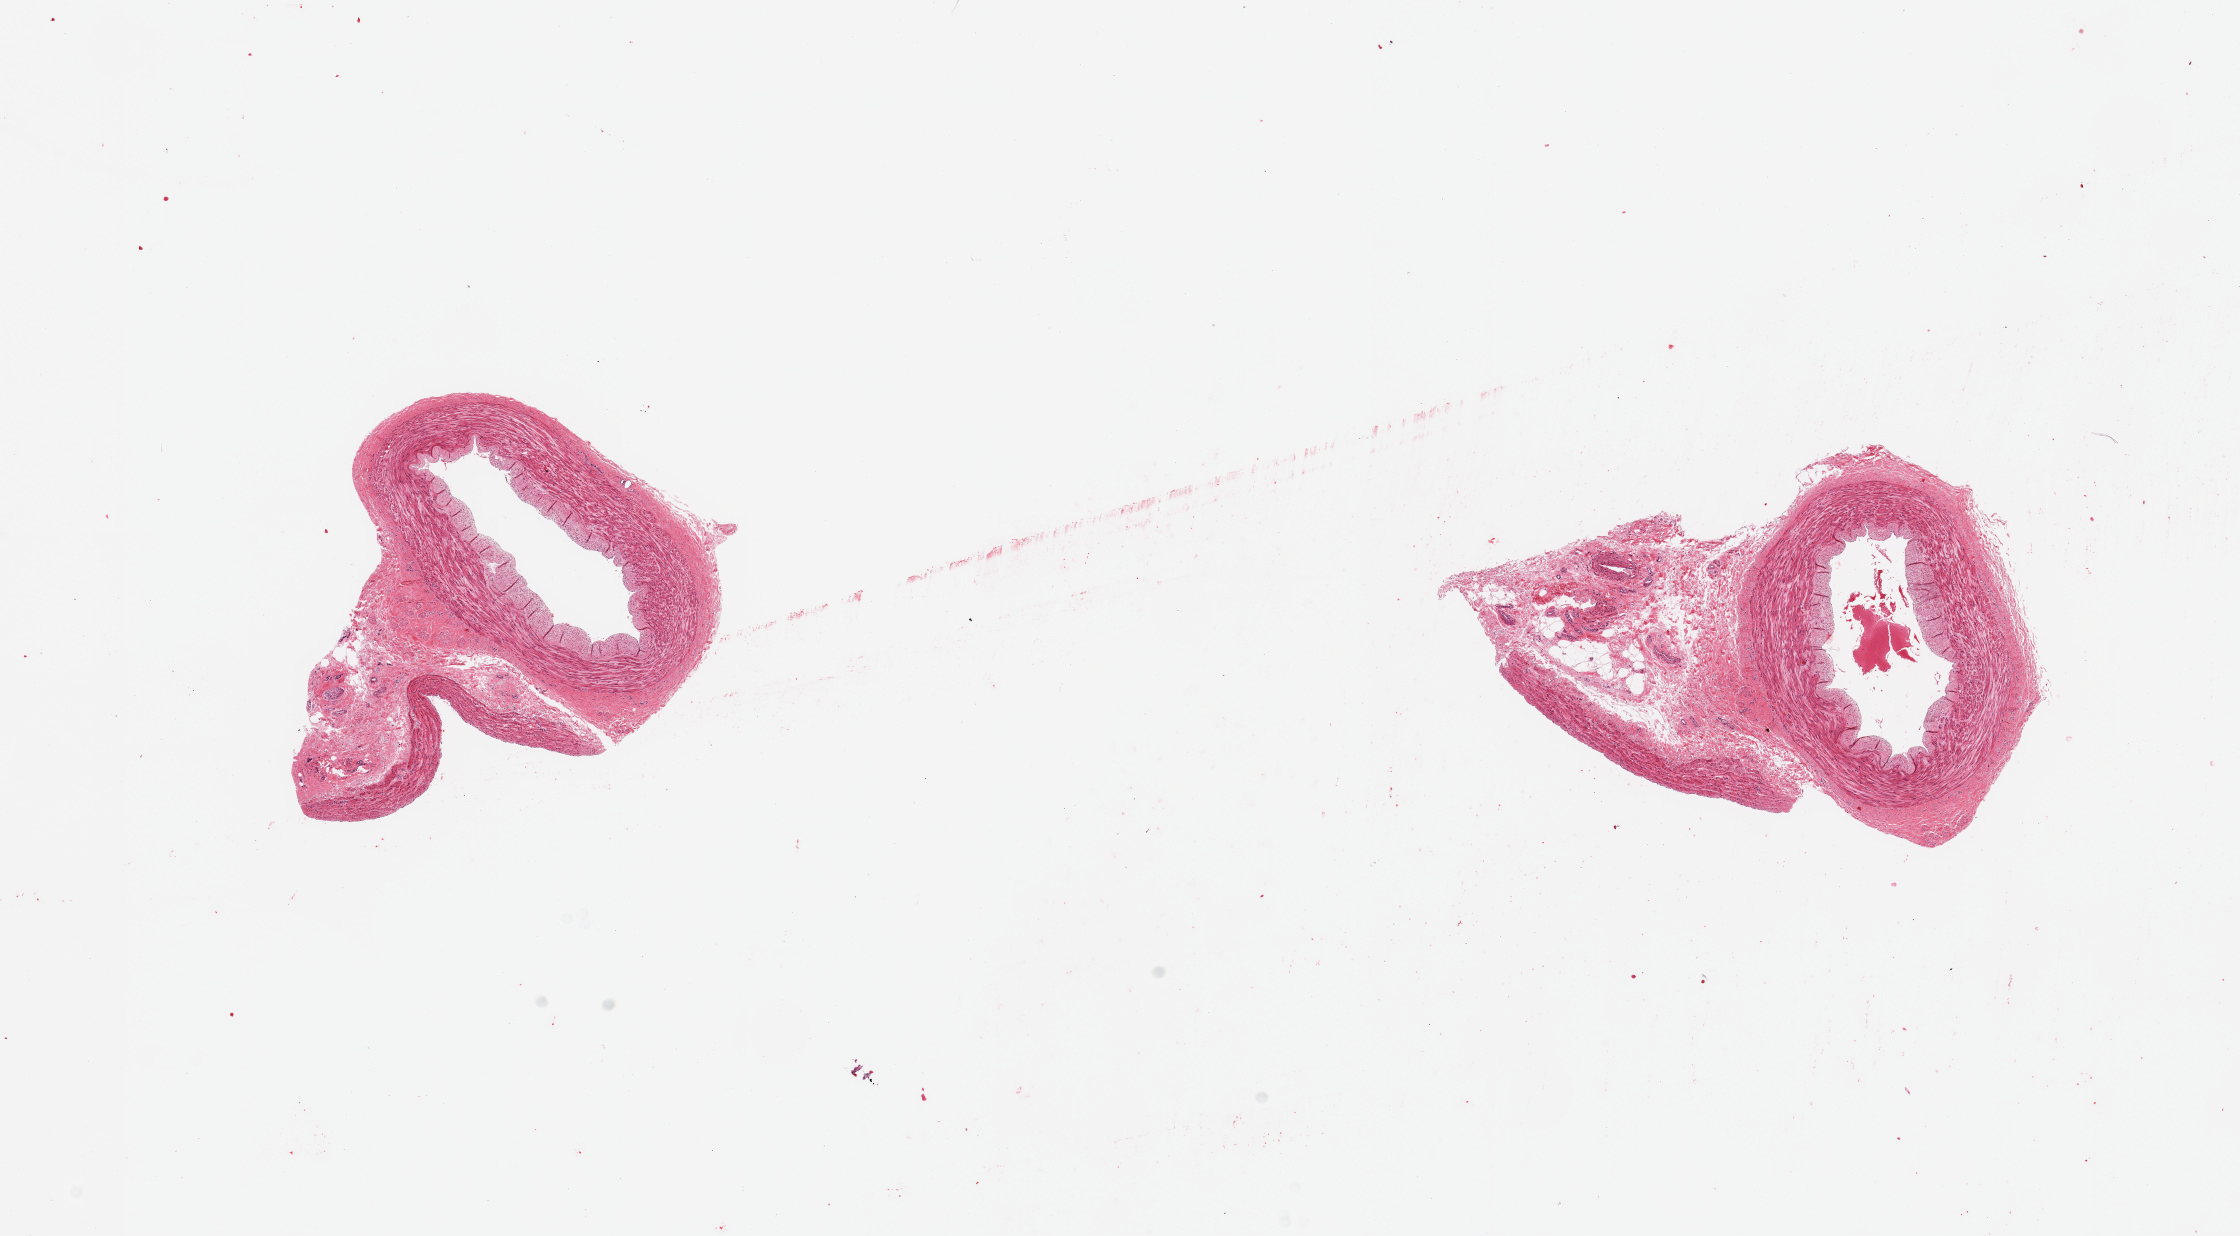
Whole-slide image, H&E stain, shown as a low-resolution overview of the whole scanned area (about 17.7 x 9.8 mm, acquisition: 20x scan). PAXgene-fixed, paraffin-embedded tissue. Section of tibial artery (target tissue). Donor tissue sample.
- reviewer comment on this tissue sample: 2 pieces; thin fibrous intimal plaques; 20% & 40% fibrofatty external stroma